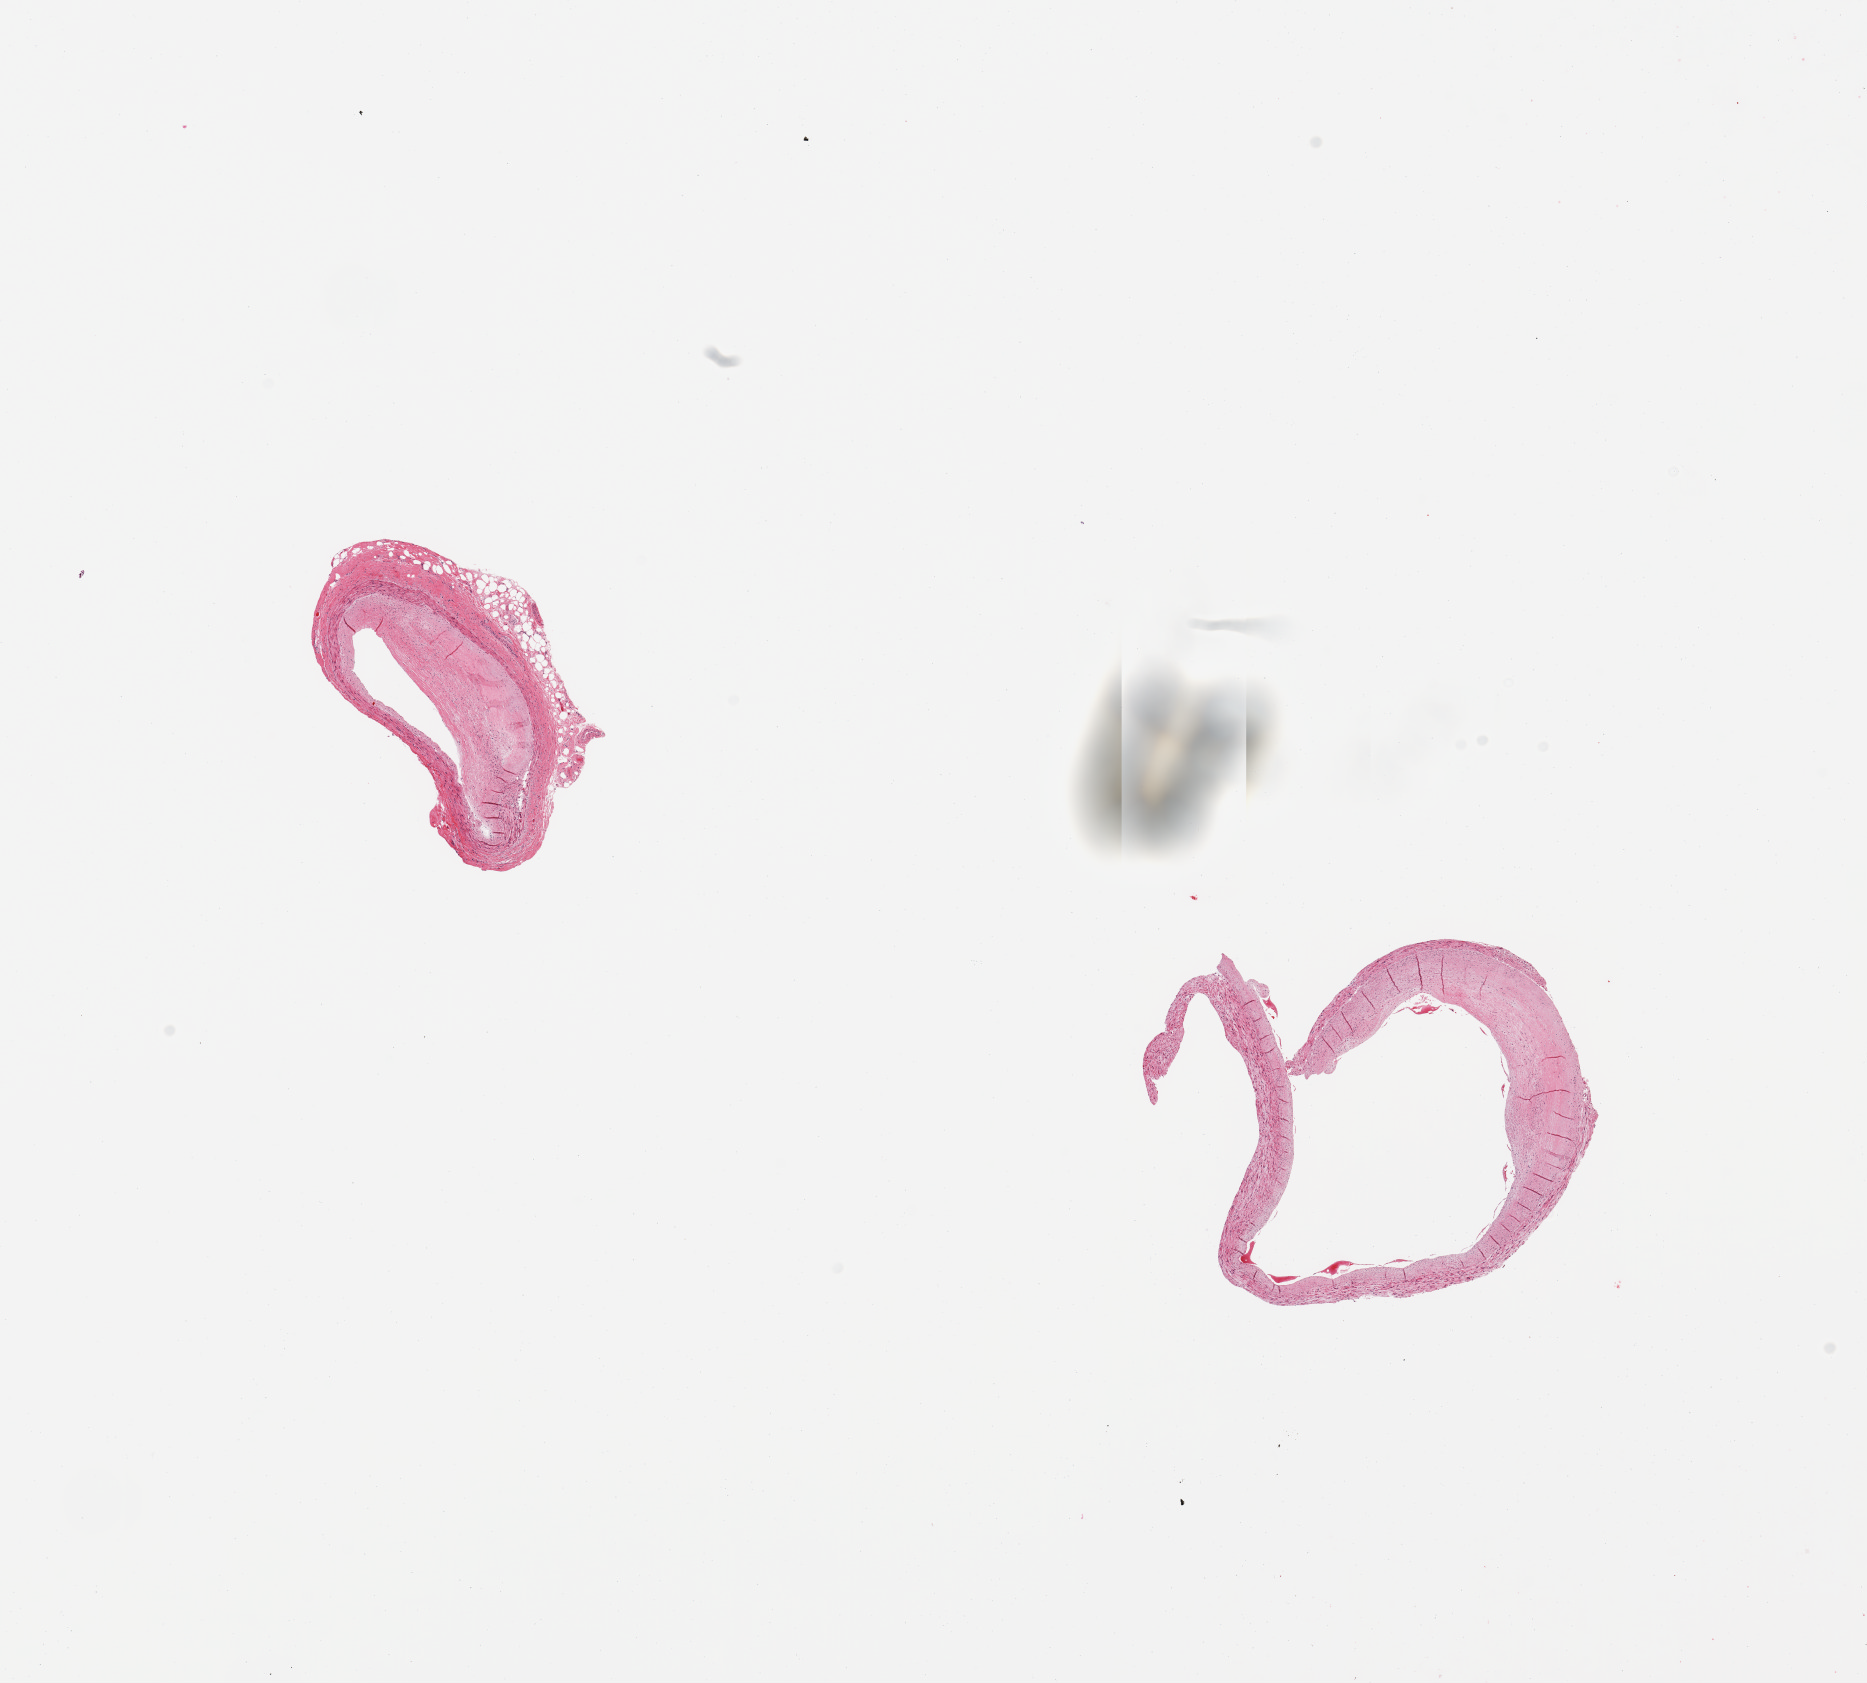
H&E whole-slide image, low-resolution overview of the scanned area, about 14.8 x 13.3 mm (from a 20x scan); PAXgene-fixed paraffin-embedded (PFPE) section; target tissue: coronary artery; donor tissue sample. Donor sex: female.
Pathologist's review note for this sample: 2 pieces, one with subtotally occlusive atherosis.